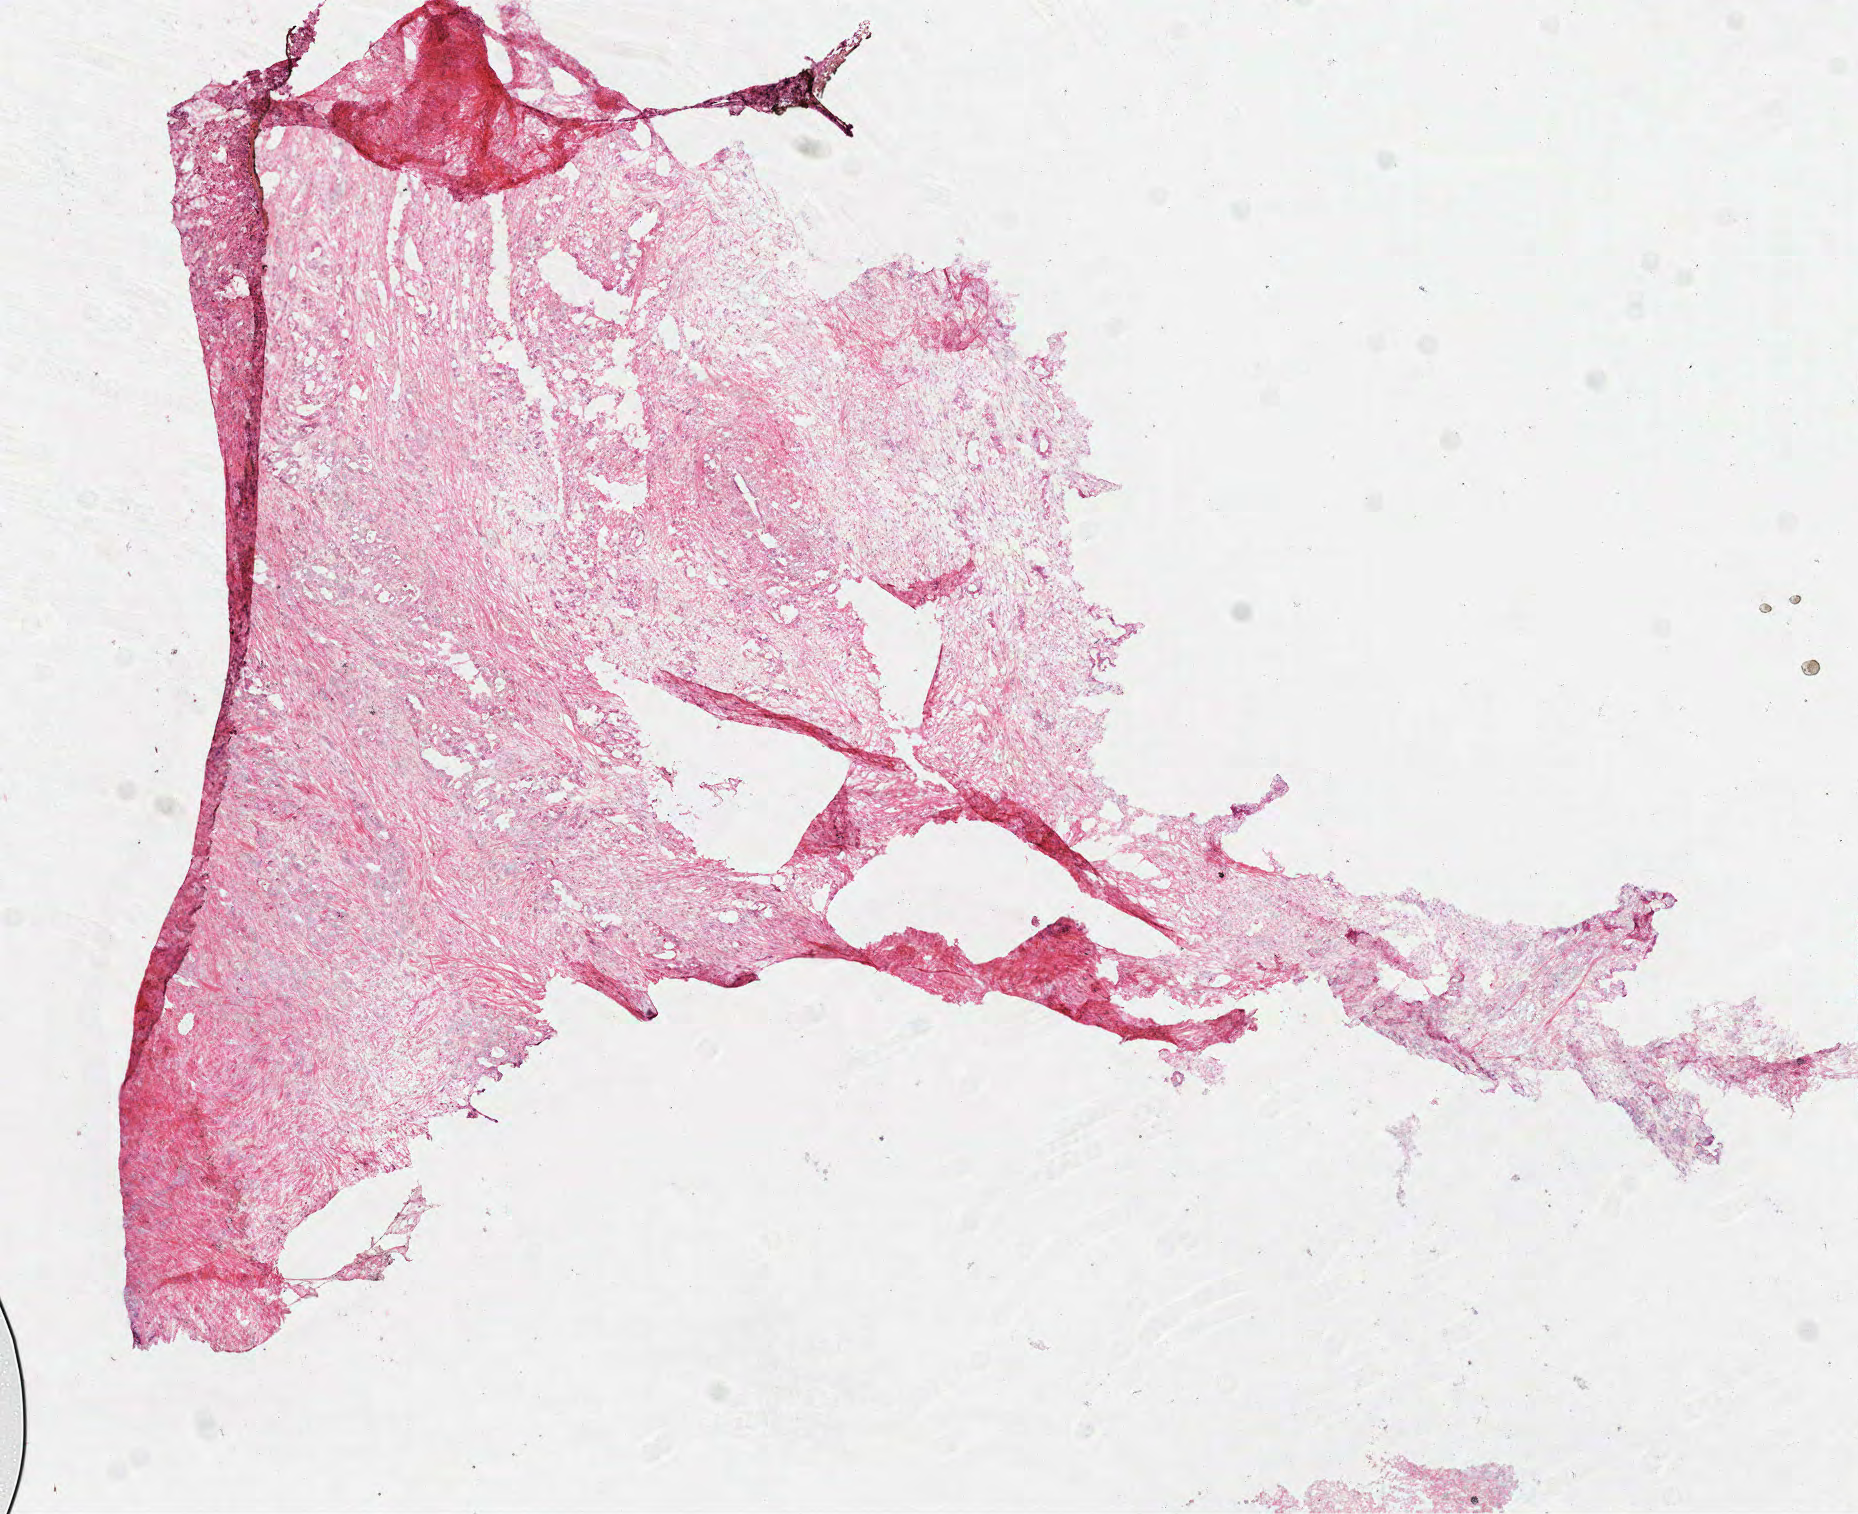
Whole-slide histology image, H&E-stained — low-resolution overview of the scanned area, about 7.5 x 6.1 mm, frozen section, pancreas, primary tumour sample. Male, age 60 years at initial diagnosis. Histologic grade: G2 (moderately differentiated). Slide review estimates, as recorded: tumour cells 90%, tumour nuclei 70%, normal cells 0%, stromal cells 10%, necrosis 0%. Inflammatory infiltration, as recorded: lymphocyte infiltration 5%, monocyte infiltration 0%, neutrophil infiltration 0%.
AJCC pathologic stage: IIB (6th edition). Pathologic diagnosis: Infiltrating duct carcinoma, NOS (head of pancreas). Lymph nodes positive (case pathology): 6 of 6 examined.